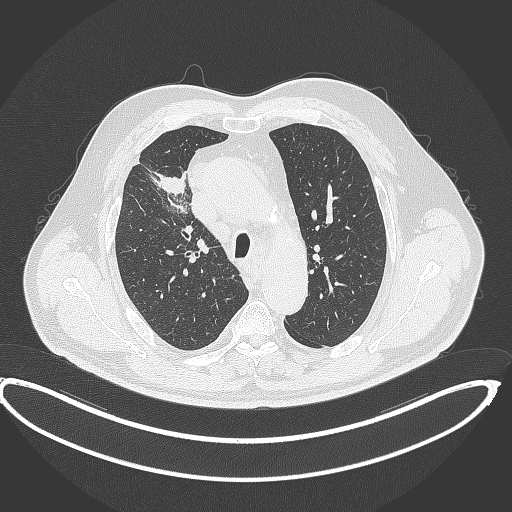
Chest CT, one axial slice; slice 296 of 390 in the series (ordered by position); reconstruction kernel B70f; 120 kVp; lung window (W 1500 / L -600 HU); 1 mm slice thickness; 512 × 512 image matrix. Male patient, age 62 years. From the clinical record (not read from this slice): clinical TNM (as recorded): T1c N3 M1c.
Structures marked on this image (rectangle marked by the reading radiologist):
- lung tumour (recorded histology: adenocarcinoma): bounding box [x1, y1, x2, y2] px = [154, 170, 187, 197]